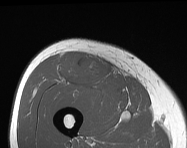
MRI of an extremity soft-tissue mass, one axial slice. Position 66 of 114 along the scan axis. MR volume resampled by the dataset authors to the PET/CT grid (not the native acquisition matrix). 3.27 mm slice thickness. 187 × 148 image matrix. Male patient. From the clinical record (not read from this slice): histological type: pleiomorphic leiomyosarcoma; grade: intermediate; site of the primary tumour: right thigh.
Annotated regions visible in this slice (expert contour drawn on MRI and transferred to this co-registered scan by the dataset authors):
- gross tumour volume including surrounding oedema: bounding box (x1, y1, x2, y2) in pixels: (59, 52, 110, 87)
- gross tumour volume (mass): (73, 61, 94, 82)